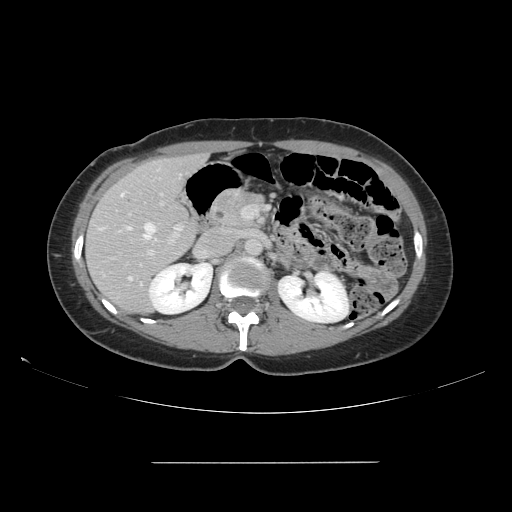
Contrast-enhanced abdominal CT, one axial slice. Slice 83 of 151 in the series (ordered by position). Soft-tissue window (W 400 / L 40 HU). 2.5 mm slice thickness. 512 × 512 image matrix, field of view 421 × 421 mm. Female patient, age 46 years. From the clinical record (not read from this slice): diagnosis: colorectal cancer liver metastases, imaged before liver resection; multiple liver metastases: yes.
Annotated regions visible in this slice (expert manual segmentation):
- hepatic veins: bounding box [x1, y1, x2, y2] px = [120, 192, 156, 279]
- liver: [87, 155, 207, 314]
- planned liver remnant (the part of the liver to remain after resection): [95, 155, 202, 313]
- portal vein (with intrahepatic branches): [128, 192, 247, 260]